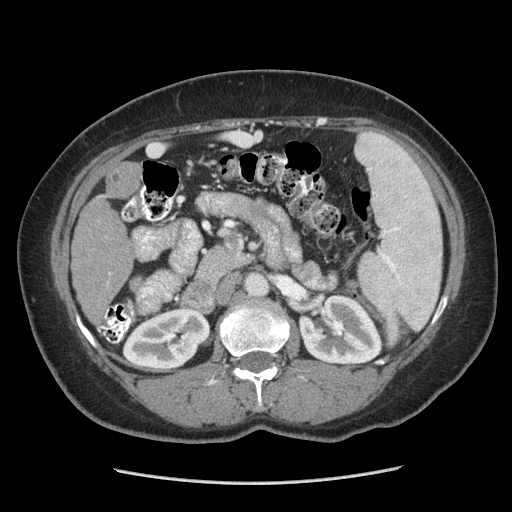
Contrast-enhanced abdominal CT (liver protocol), one axial slice. Slice 129 of 185 in the series (ordered by position). Reconstruction kernel STANDARD. 140 kVp. Soft-tissue window (W 400 / L 40 HU). 2.5 mm slice thickness. 512 × 512 image matrix. From the clinical record (not read from this slice): diagnosis: hepatocellular carcinoma (patient treated with transarterial chemoembolisation; whether this scan precedes or follows treatment is not stated here); TNM stage (as recorded): Stage-I; Child-Pugh class: A; tumour differentiation: poorly differentiated; tumour nodularity: uninodular.
Annotated regions visible in this slice (semi-automatic segmentation, software-assisted and operator-edited):
- liver parenchyma outside the tumour (the mass and vessels are separate outlines, so this box may not span the whole liver): bounding box [x1, y1, x2, y2] px = [71, 194, 134, 316]
- mass: [108, 163, 140, 197]